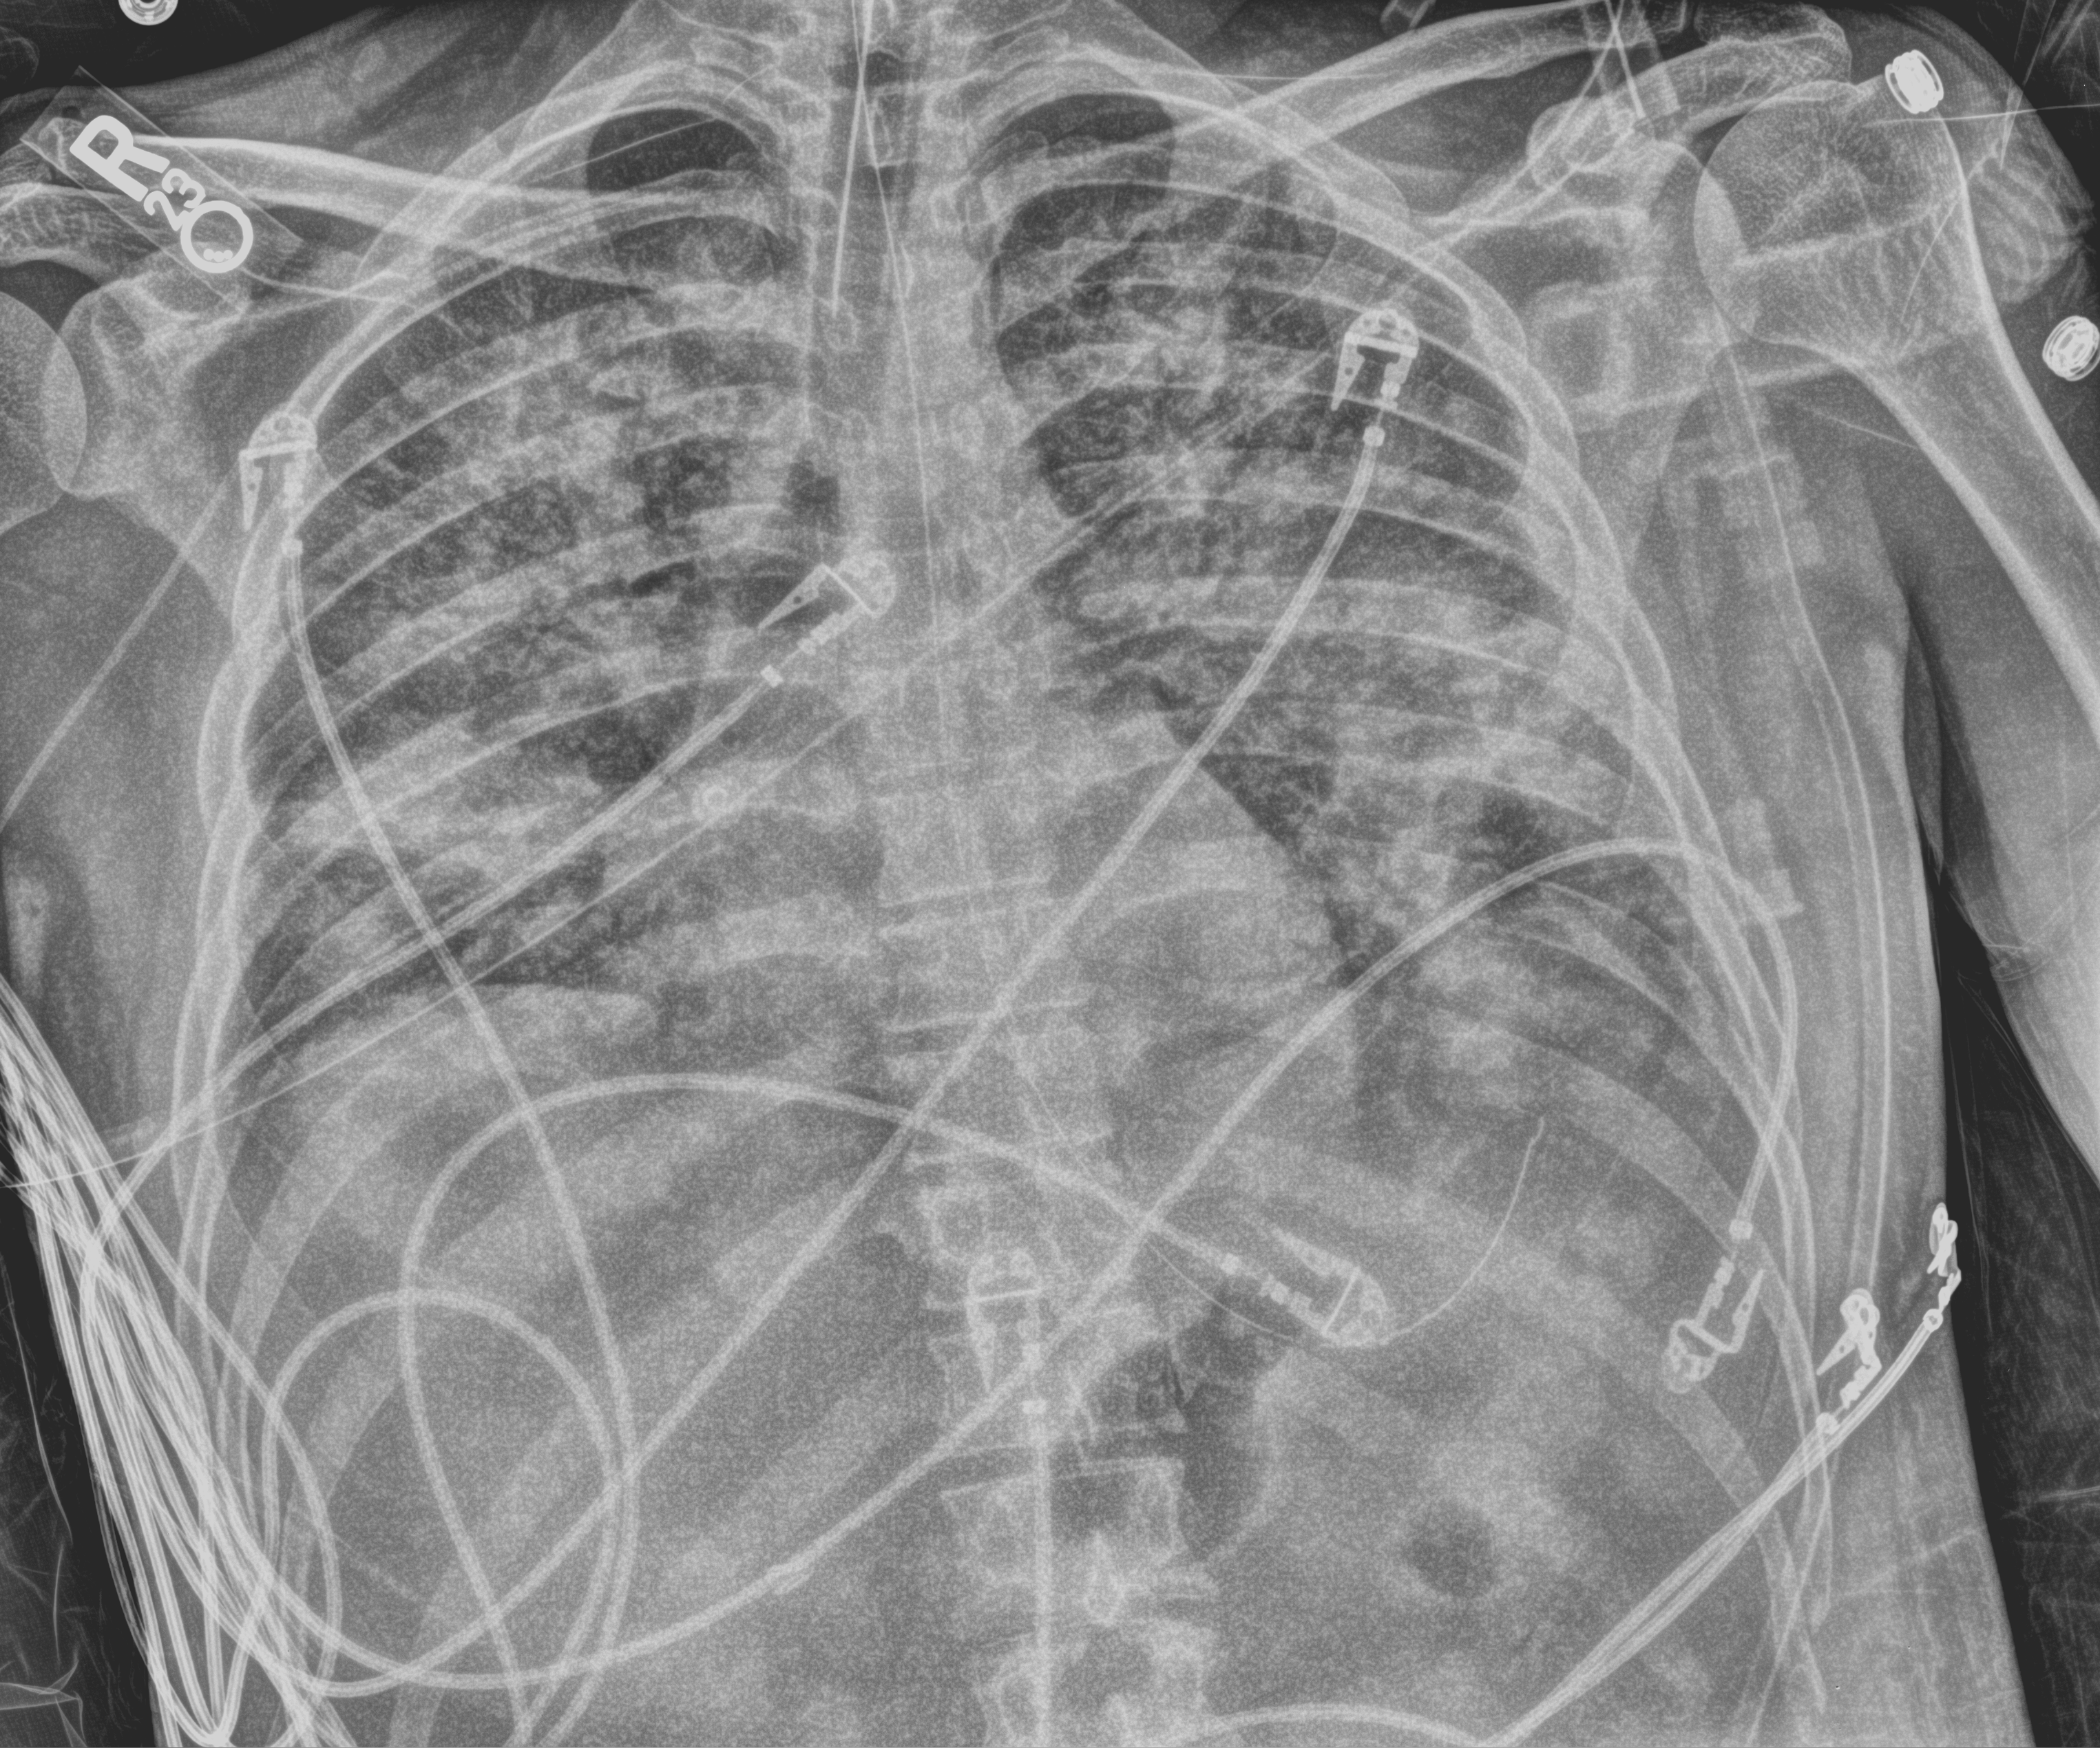
Chest X-ray (portable). Patient hospitalised with COVID-19; male, aged 18–59 years.
From the hospital-stay record, not from the radiograph (when in the stay this image was taken is not recorded): smoking status (admission record): never.